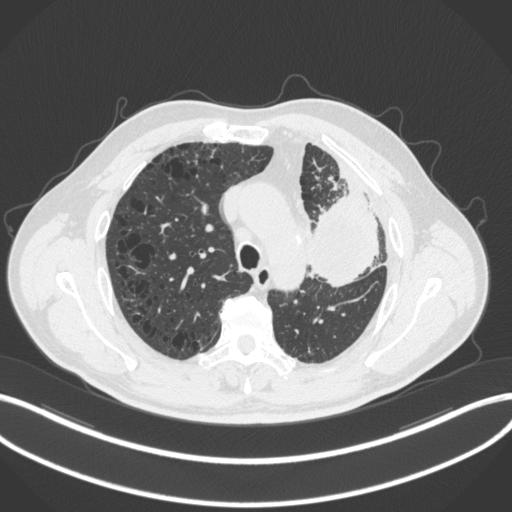
Chest CT, one axial slice; position 214 of 286 along the scan axis; reconstruction kernel B31f; 120 kVp; lung window (W 1500 / L -600 HU); 1 mm slice thickness; 512 × 512 image matrix. Male patient, age 68 years. Case-level facts recorded for this patient, not image findings: clinical TNM (as recorded): T3 N3 M1.
Annotated regions visible in this slice (bounding box drawn by a radiologist):
- lung tumour (recorded histology: adenocarcinoma): box from (x=308, y=184) to (x=384, y=289) px